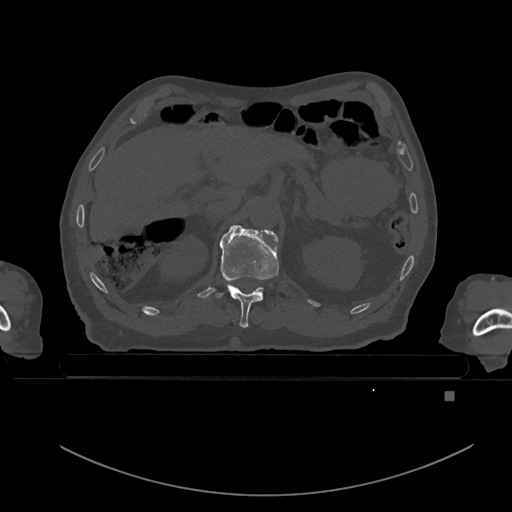
CT including the spine, one axial slice. Slice 13 of 969 in the series (ordered by position). Bone window (W 1800 / L 400 HU). 0.5 mm slice thickness. 512 × 512 image matrix, field of view 456 × 456 mm. Patient: male, 82 years. Case-level facts recorded for this patient, not image findings: primary cancer: prostate; vertebrae with lytic lesions (as recorded): T11, T9, T8, T2.
Structures marked on this image (semi-automatic segmentation, software-assisted and operator-edited):
- T11 vertebra: bounding box [x1, y1, x2, y2] px = [215, 227, 279, 328]